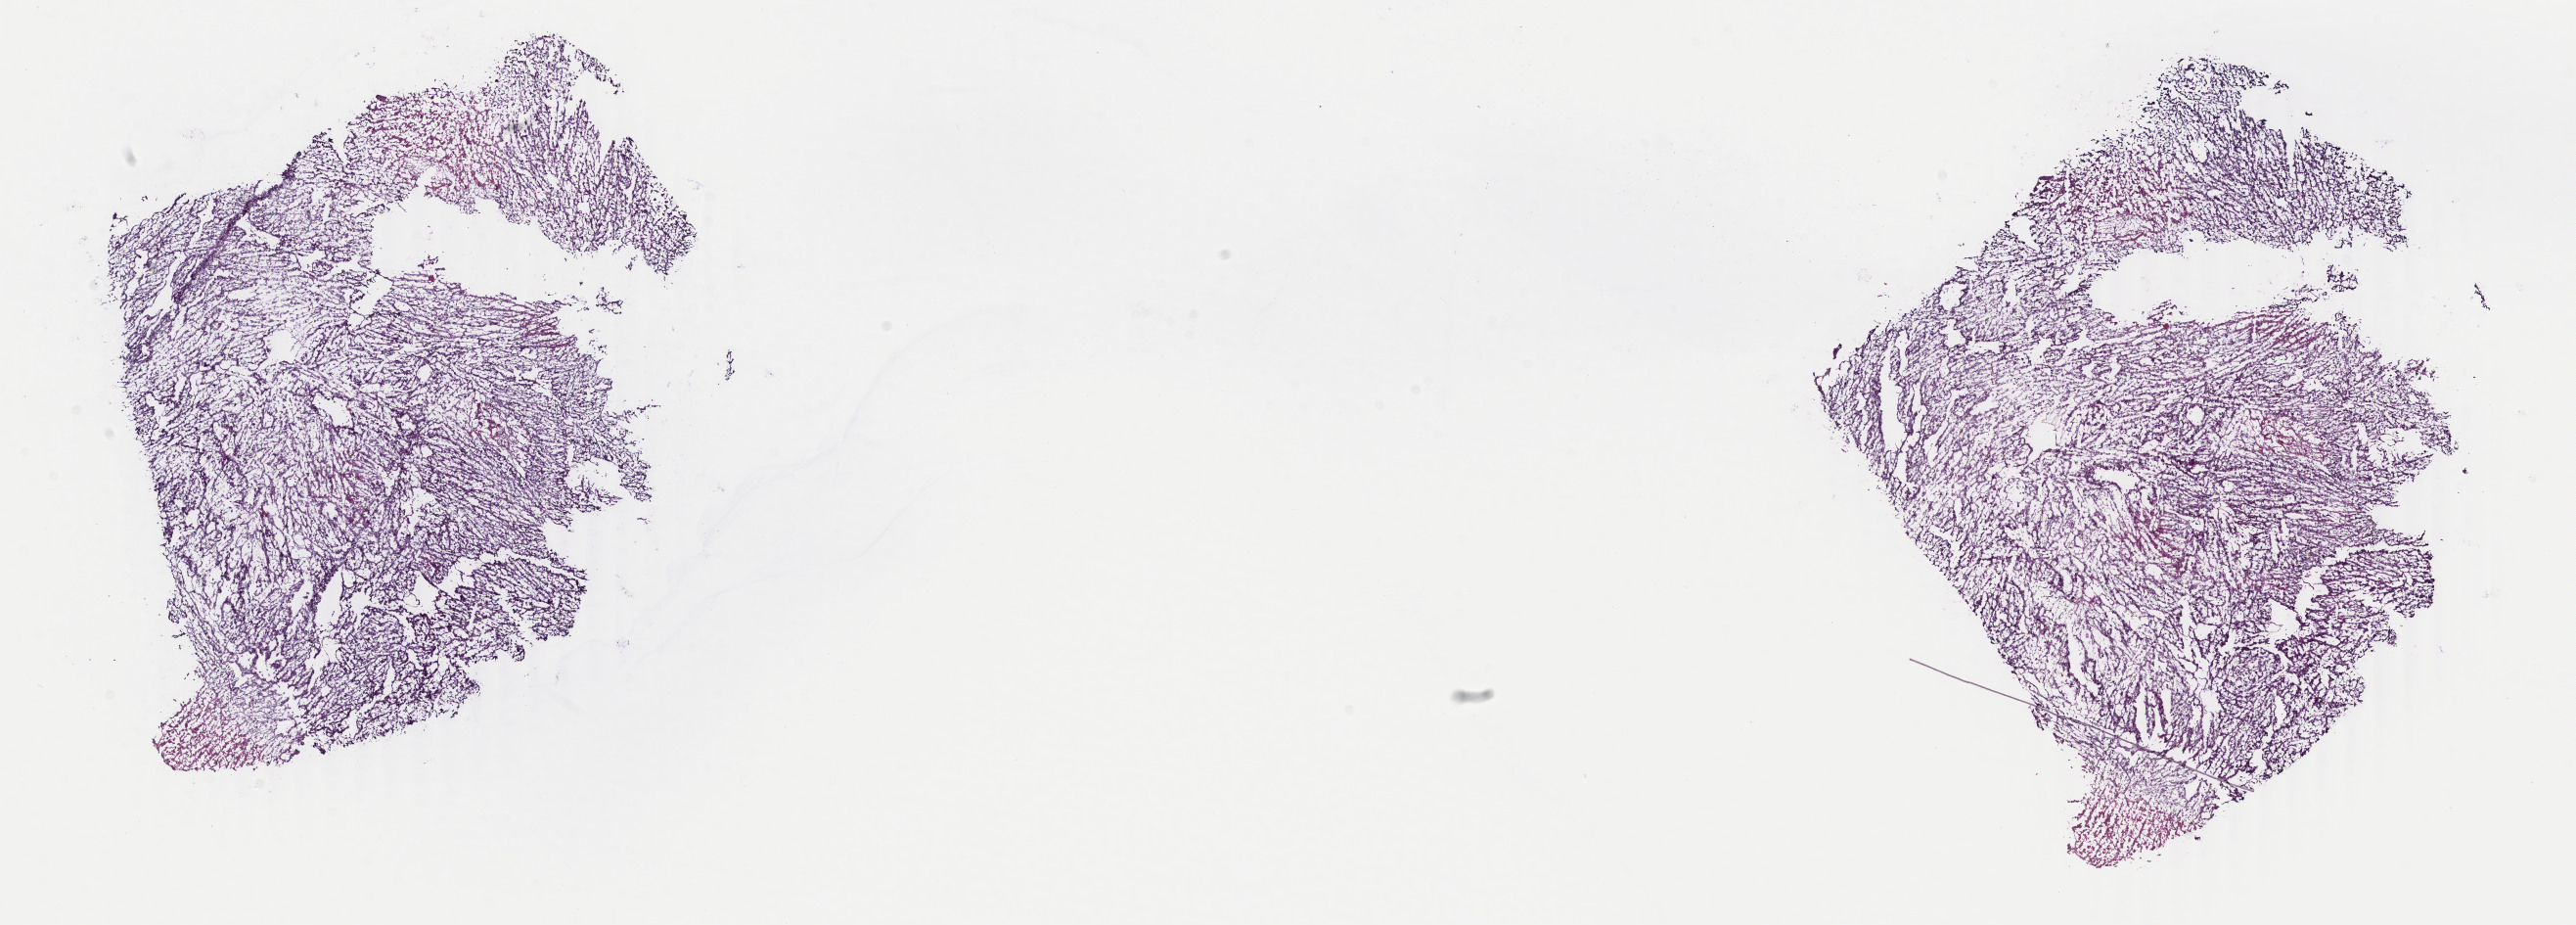
Digitized Hematoxylin and eosin (H&E) stained tissue section (whole slide), shown as a low-resolution overview of the whole scanned area (about 20.9 x 7.5 mm, acquisition: 40x scan). Frozen section from the top of the tissue portion. Sample: primary tumour, adrenal cortex. Female, age 44 years at initial diagnosis.
Histologic diagnosis: Adrenal cortical carcinoma (cortex of adrenal gland).